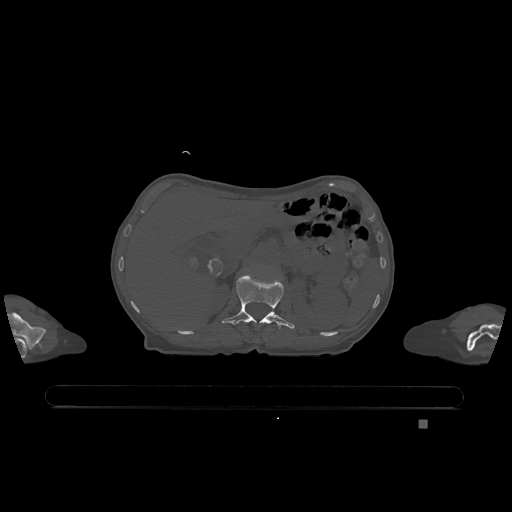
CT including the spine, one axial slice. Slice 473 of 1317 in the series (ordered by position). Bone window (W 1800 / L 400 HU). 512 × 512 image matrix, field of view 500 × 500 mm. Female patient, age 74 years. From the clinical record (not read from this slice): primary cancer: lung; vertebrae with lytic lesions (as recorded): T1, T4, T5, T6, L4, L5.
Outlined on this slice (semi-automatic segmentation, software-assisted and operator-edited):
- L1 vertebra: bounding box <222,273,295,329> (left, top, right, bottom; pixels)